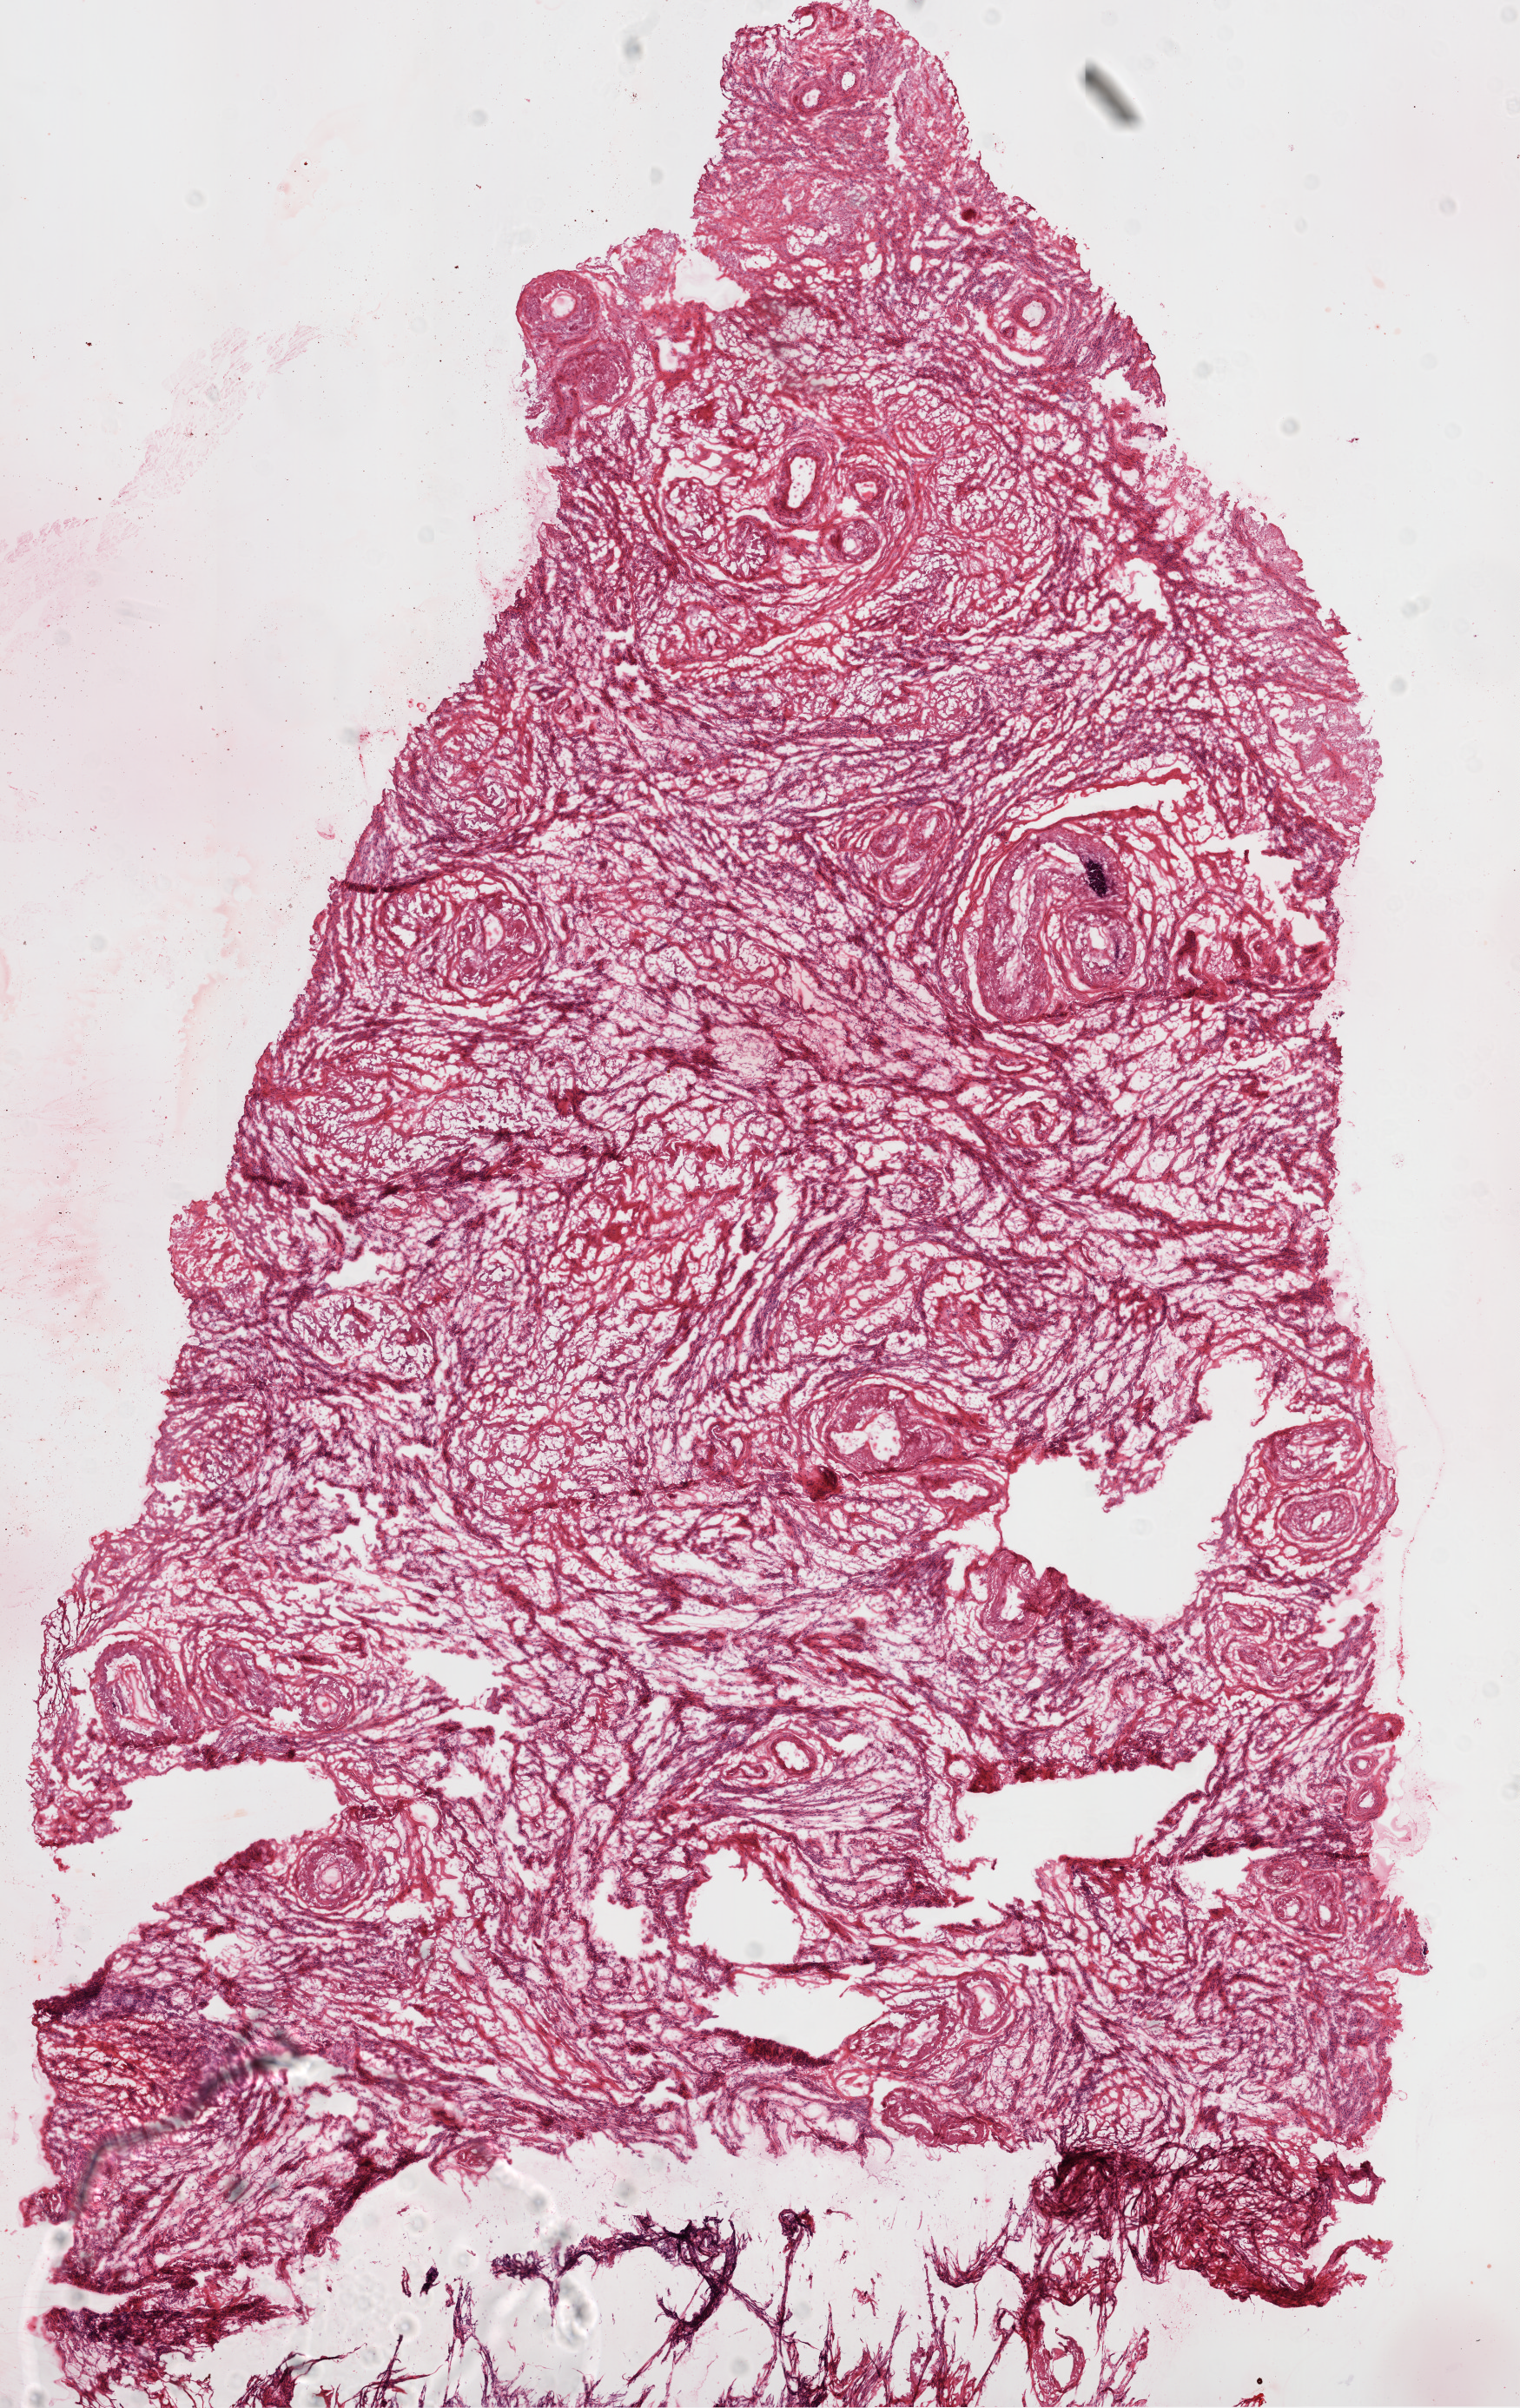
H&E-stained whole-slide image — low-resolution overview of the scanned area, about 7.0 x 11.1 mm (from a 20x scan); frozen section from the top of the tissue portion; ovary, solid tissue normal (non-tumour tissue) sample. Female, age 71 years at initial diagnosis.
* this section: solid tissue normal (non-tumour) sample from the same patient
* patient diagnosis: Serous cystadenocarcinoma, NOS